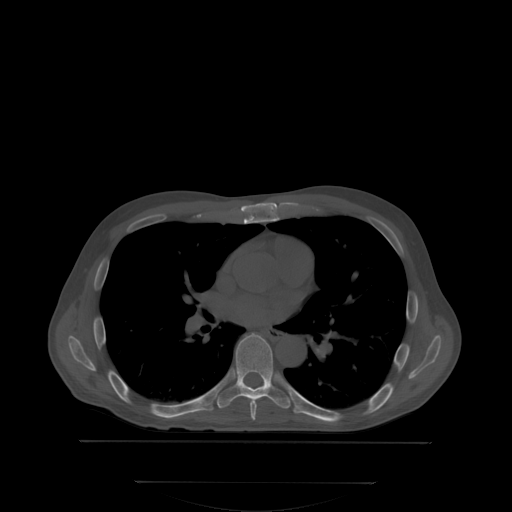
CT including the spine, one axial slice. Slice 228 of 350 in the series (ordered by position). Bone window (W 1800 / L 400 HU). 512 × 512 image matrix, field of view 500 × 500 mm. Patient: male, 58 years. Case-level facts recorded for this patient, not image findings: primary cancer: prostate.
Annotated regions visible in this slice (semi-automatically segmented with operator editing):
- T6 vertebra: bounding box (x1, y1, x2, y2) in pixels: (250, 402, 257, 419)
- T7 vertebra: (217, 333, 291, 407)